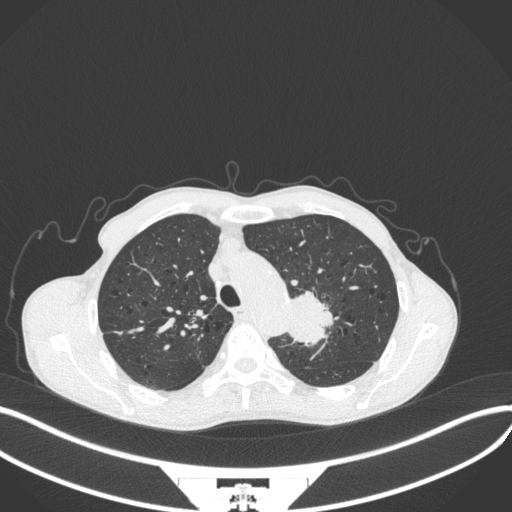
Chest CT, one axial slice; slice 318 of 394 in the series (ordered by position); lung window (W 1500 / L -600 HU); 1 mm slice thickness; 512 × 512 image matrix, field of view 400 × 400 mm. Male patient, age 65 years. From the clinical record (not read from this slice): clinical TNM (as recorded): T2b N0 M0; histopathological grade: G2.
Annotated regions visible in this slice (rectangle marked by the reading radiologist):
- lung tumour (recorded histology: adenocarcinoma): bounding box [x1, y1, x2, y2] px = [279, 287, 336, 347]